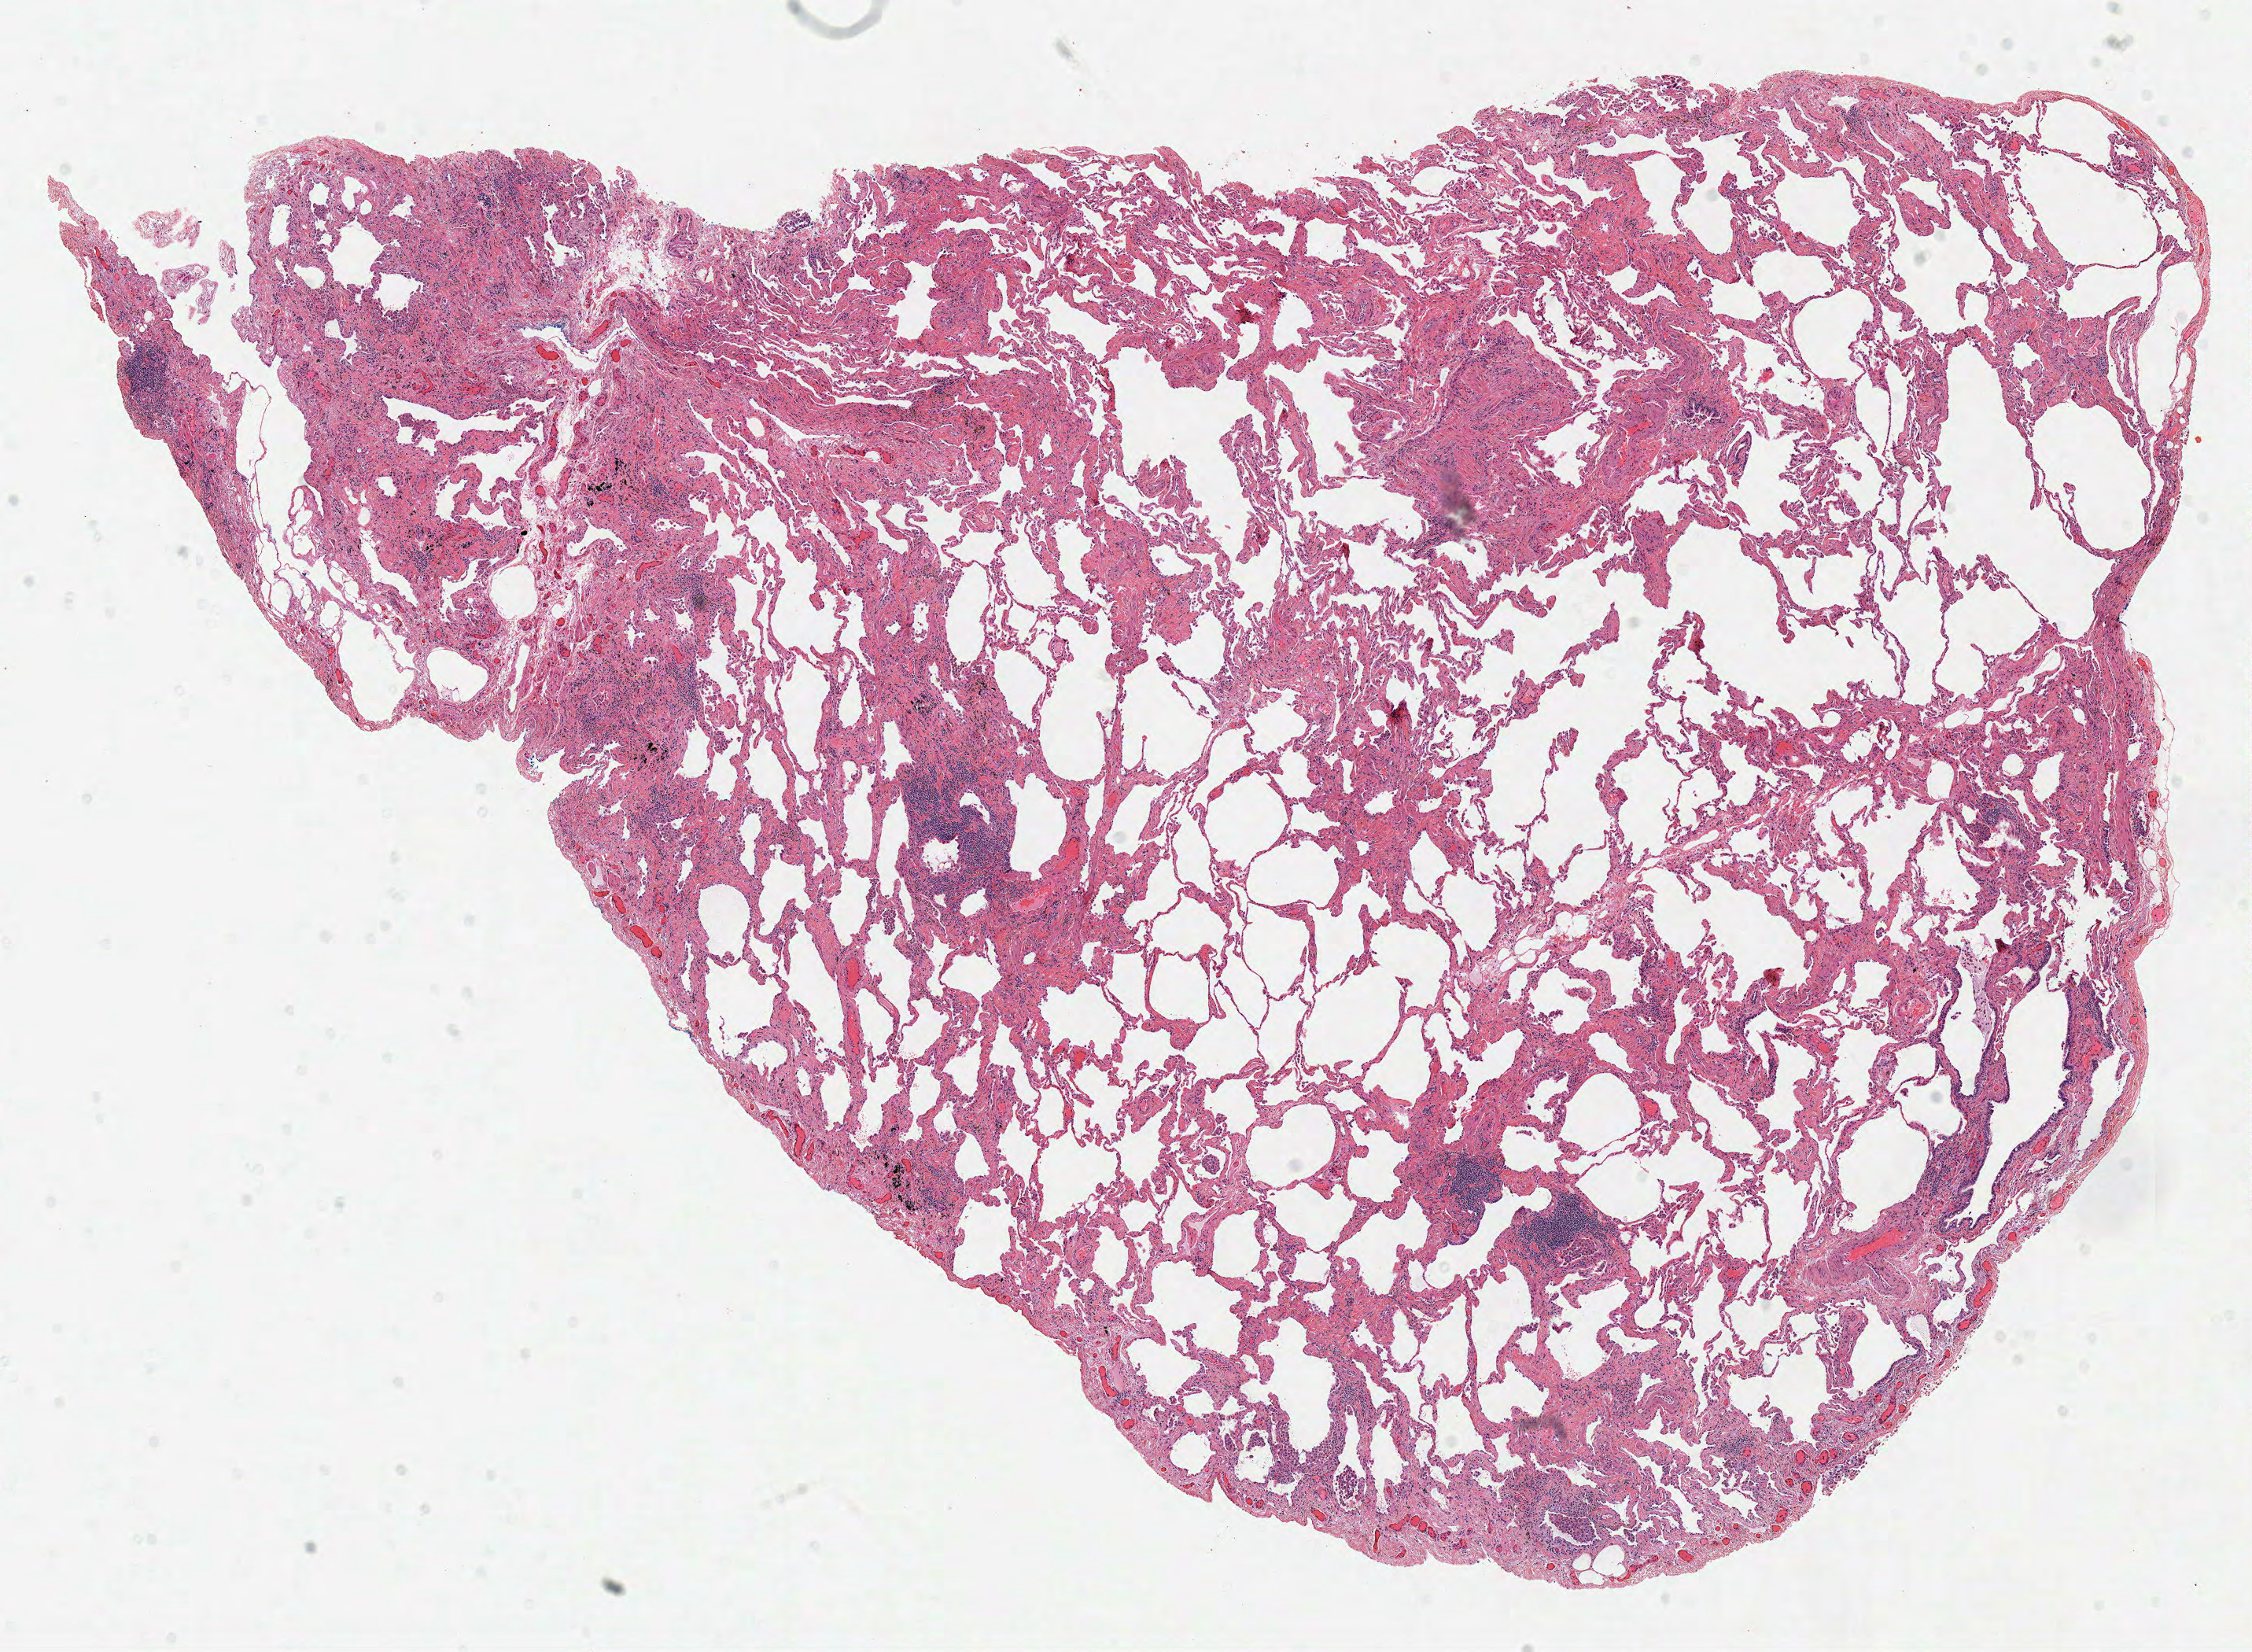
H&E whole-slide image, low-resolution overview of the scanned area, about 11.3 x 8.3 mm. Frozen section from the top of the tissue portion. Lung, solid tissue normal (non-tumour tissue) sample. Patient: female, age at initial diagnosis 85 years.
This section: solid tissue normal sample (biorepository sample class). Patient diagnosis: Adenocarcinoma, NOS (upper lobe, lung).